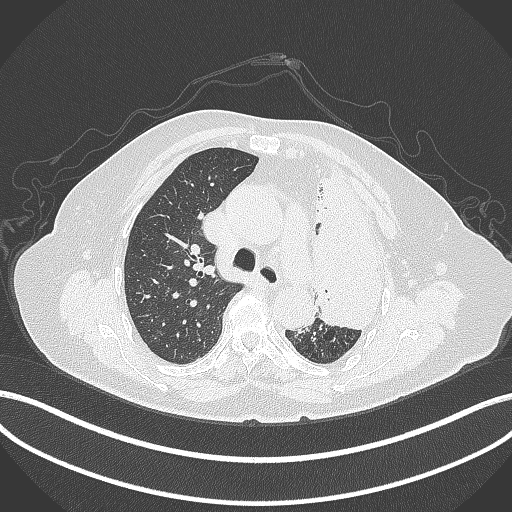
Chest CT, one axial slice; slice 271 of 399 in the series (ordered by position); 120 kVp; lung window (W 1500 / L -600 HU); 1 mm slice thickness; 512 × 512 image matrix, field of view 400 × 400 mm. Female patient, age 75 years. From the clinical record (not read from this slice): clinical TNM (as recorded): T3 N3 M1.
Outlined on this slice (rectangle marked by the reading radiologist):
- lung tumour (recorded histology: adenocarcinoma): bounding box <302,161,394,339> (left, top, right, bottom; pixels)